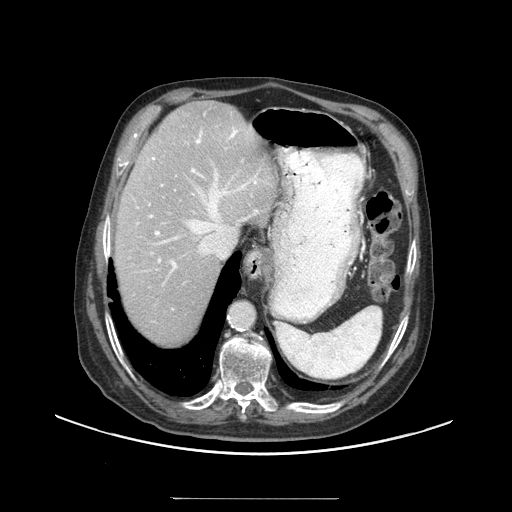
Contrast-enhanced abdominal CT (liver protocol), one axial slice. Reconstruction kernel STANDARD. 140 kVp. Soft-tissue window (W 400 / L 40 HU). 512 × 512 image matrix, field of view 450 × 450 mm. Case-level facts recorded for this patient, not image findings: diagnosis: hepatocellular carcinoma (patient treated with transarterial chemoembolisation; whether this scan precedes or follows treatment is not stated here); TNM stage (as recorded): Stage-IIIC; Child-Pugh class: A; tumour differentiation: well differentiated; tumour nodularity: uninodular.
Structures marked on this image (semi-automatically segmented with operator editing):
- abdominal aorta: bounding box [x1, y1, x2, y2] px = [230, 301, 256, 329]
- liver parenchyma outside the tumour (the mass and vessels are separate outlines, so this box may not span the whole liver): [114, 100, 276, 344]
- liver vessels: [133, 128, 259, 310]